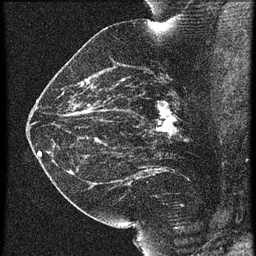
Breast MRI (dynamic contrast-enhanced), one sagittal slice. Position 33 of 60 along the scan axis. 3 images stored at this slice position (order not interpretable as contrast timing). 1.5 T. TE 4.2 ms, TR 21.3 ms. 1.5 mm slice thickness. 256 × 256 image matrix, field of view 180 × 180 mm. Female patient, age 42 years. Case-level facts recorded for this patient, not image findings: setting: breast cancer imaged before/during neoadjuvant chemotherapy; receptor status: HER2-positive.
Annotated regions visible in this slice (semi-automatically segmented with operator editing):
- analysis volume of interest (the breast-tissue region the enhancement analysis was run in; not a lesion): bounding box [x1, y1, x2, y2] px = [122, 82, 195, 147]
- tumour enhancement mask (voxels above the 90 % enhancement threshold inside the analysis volume of interest): [156, 102, 175, 133]